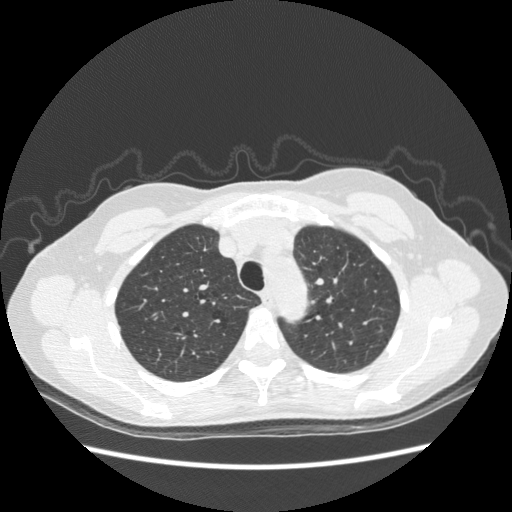
Chest CT (low-dose screening protocol), one axial image. Baseline screening round. Lung window (W 1500 / L -600 HU). 1.25 mm slice thickness. Slice 69 of 270 in the series. Female participant, aged 61 years at enrolment. Former smoker at enrolment.
Lesion marked by an expert reader, bounding box (x1, y1, x2, y2) in pixels: (358, 319, 388, 350). Screening reader's record for this exam (one nodule recorded; not confirmed to be the boxed lesion): non-calcified nodule or mass ≥4 mm, left upper lobe, 7 × 6 mm, poorly defined margins, ground glass attenuation. Later outcome: lung cancer diagnosed 484 days after this screen — bronchiolo-alveolar adenocarcinoma, NOS, left upper lobe, well differentiated (G1), stage IA (AJCC 6th edition), 8 mm at pathology.